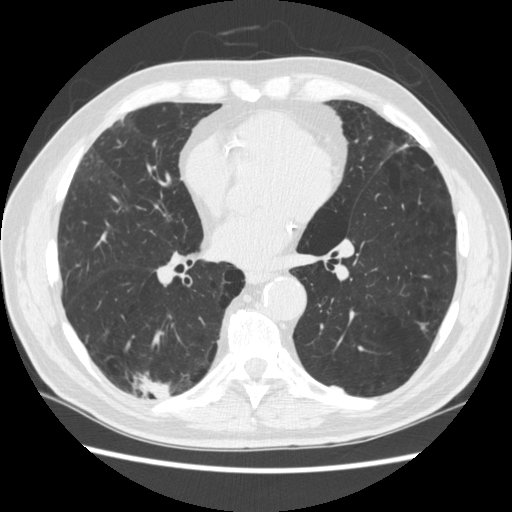
Chest CT (low-dose screening protocol), one axial image, third annual screen, lung window (W 1500 / L -600 HU), standard (soft-tissue) reconstruction kernel (STANDARD), 120 kVp, slice 145 of 266 in the series. Male, age 70 years at enrolment.
• Expert reader's lesion annotation, box from (x=122, y=361) to (x=183, y=420) px.
• The screening reader recorded 4 non-calcified nodules or masses ≥4 mm on this exam (right lower lobe, right lower lobe, left lower lobe, left lower lobe); which of them this box marks is not recorded.
• Official screen result: positive, other.
• Participant outcome: lung cancer diagnosed 253 days after this screen — squamous cell carcinoma, NOS, right upper lobe, poorly differentiated (G3), stage IV (AJCC 6th edition).